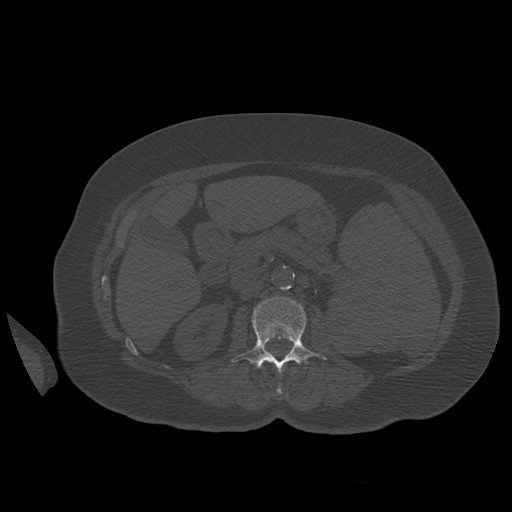
CT including the spine, one axial slice; slice 255 of 399 in the series (ordered by position); reconstruction kernel STANDARD; bone window (W 1800 / L 400 HU); 1.25 mm slice thickness; 512 × 512 image matrix, field of view 404 × 404 mm. Patient age 81 years. From the clinical record (not read from this slice): primary cancer: renal; vertebrae with lytic lesions (as recorded): L1.
Structures marked on this image (semi-automatically segmented with operator editing):
- L2 vertebra: bounding box (x1, y1, x2, y2) in pixels: (232, 297, 327, 394)